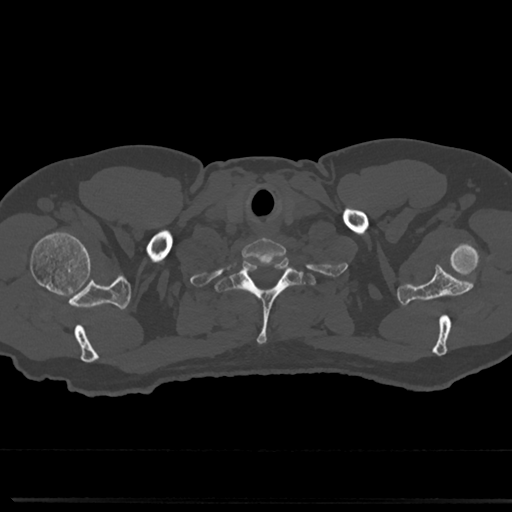
CT including the spine, one axial slice; position 681 of 817 along the scan axis; reconstruction kernel Br40s/3; bone window (W 1800 / L 400 HU); 0.5 mm slice thickness; 512 × 512 image matrix. Male patient, age 61 years. Case-level facts recorded for this patient, not image findings: primary cancer: prostate.
Outlined on this slice (semi-automatically segmented with operator editing):
- T1 vertebra: bounding box (x1, y1, x2, y2) in pixels: (222, 253, 310, 345)